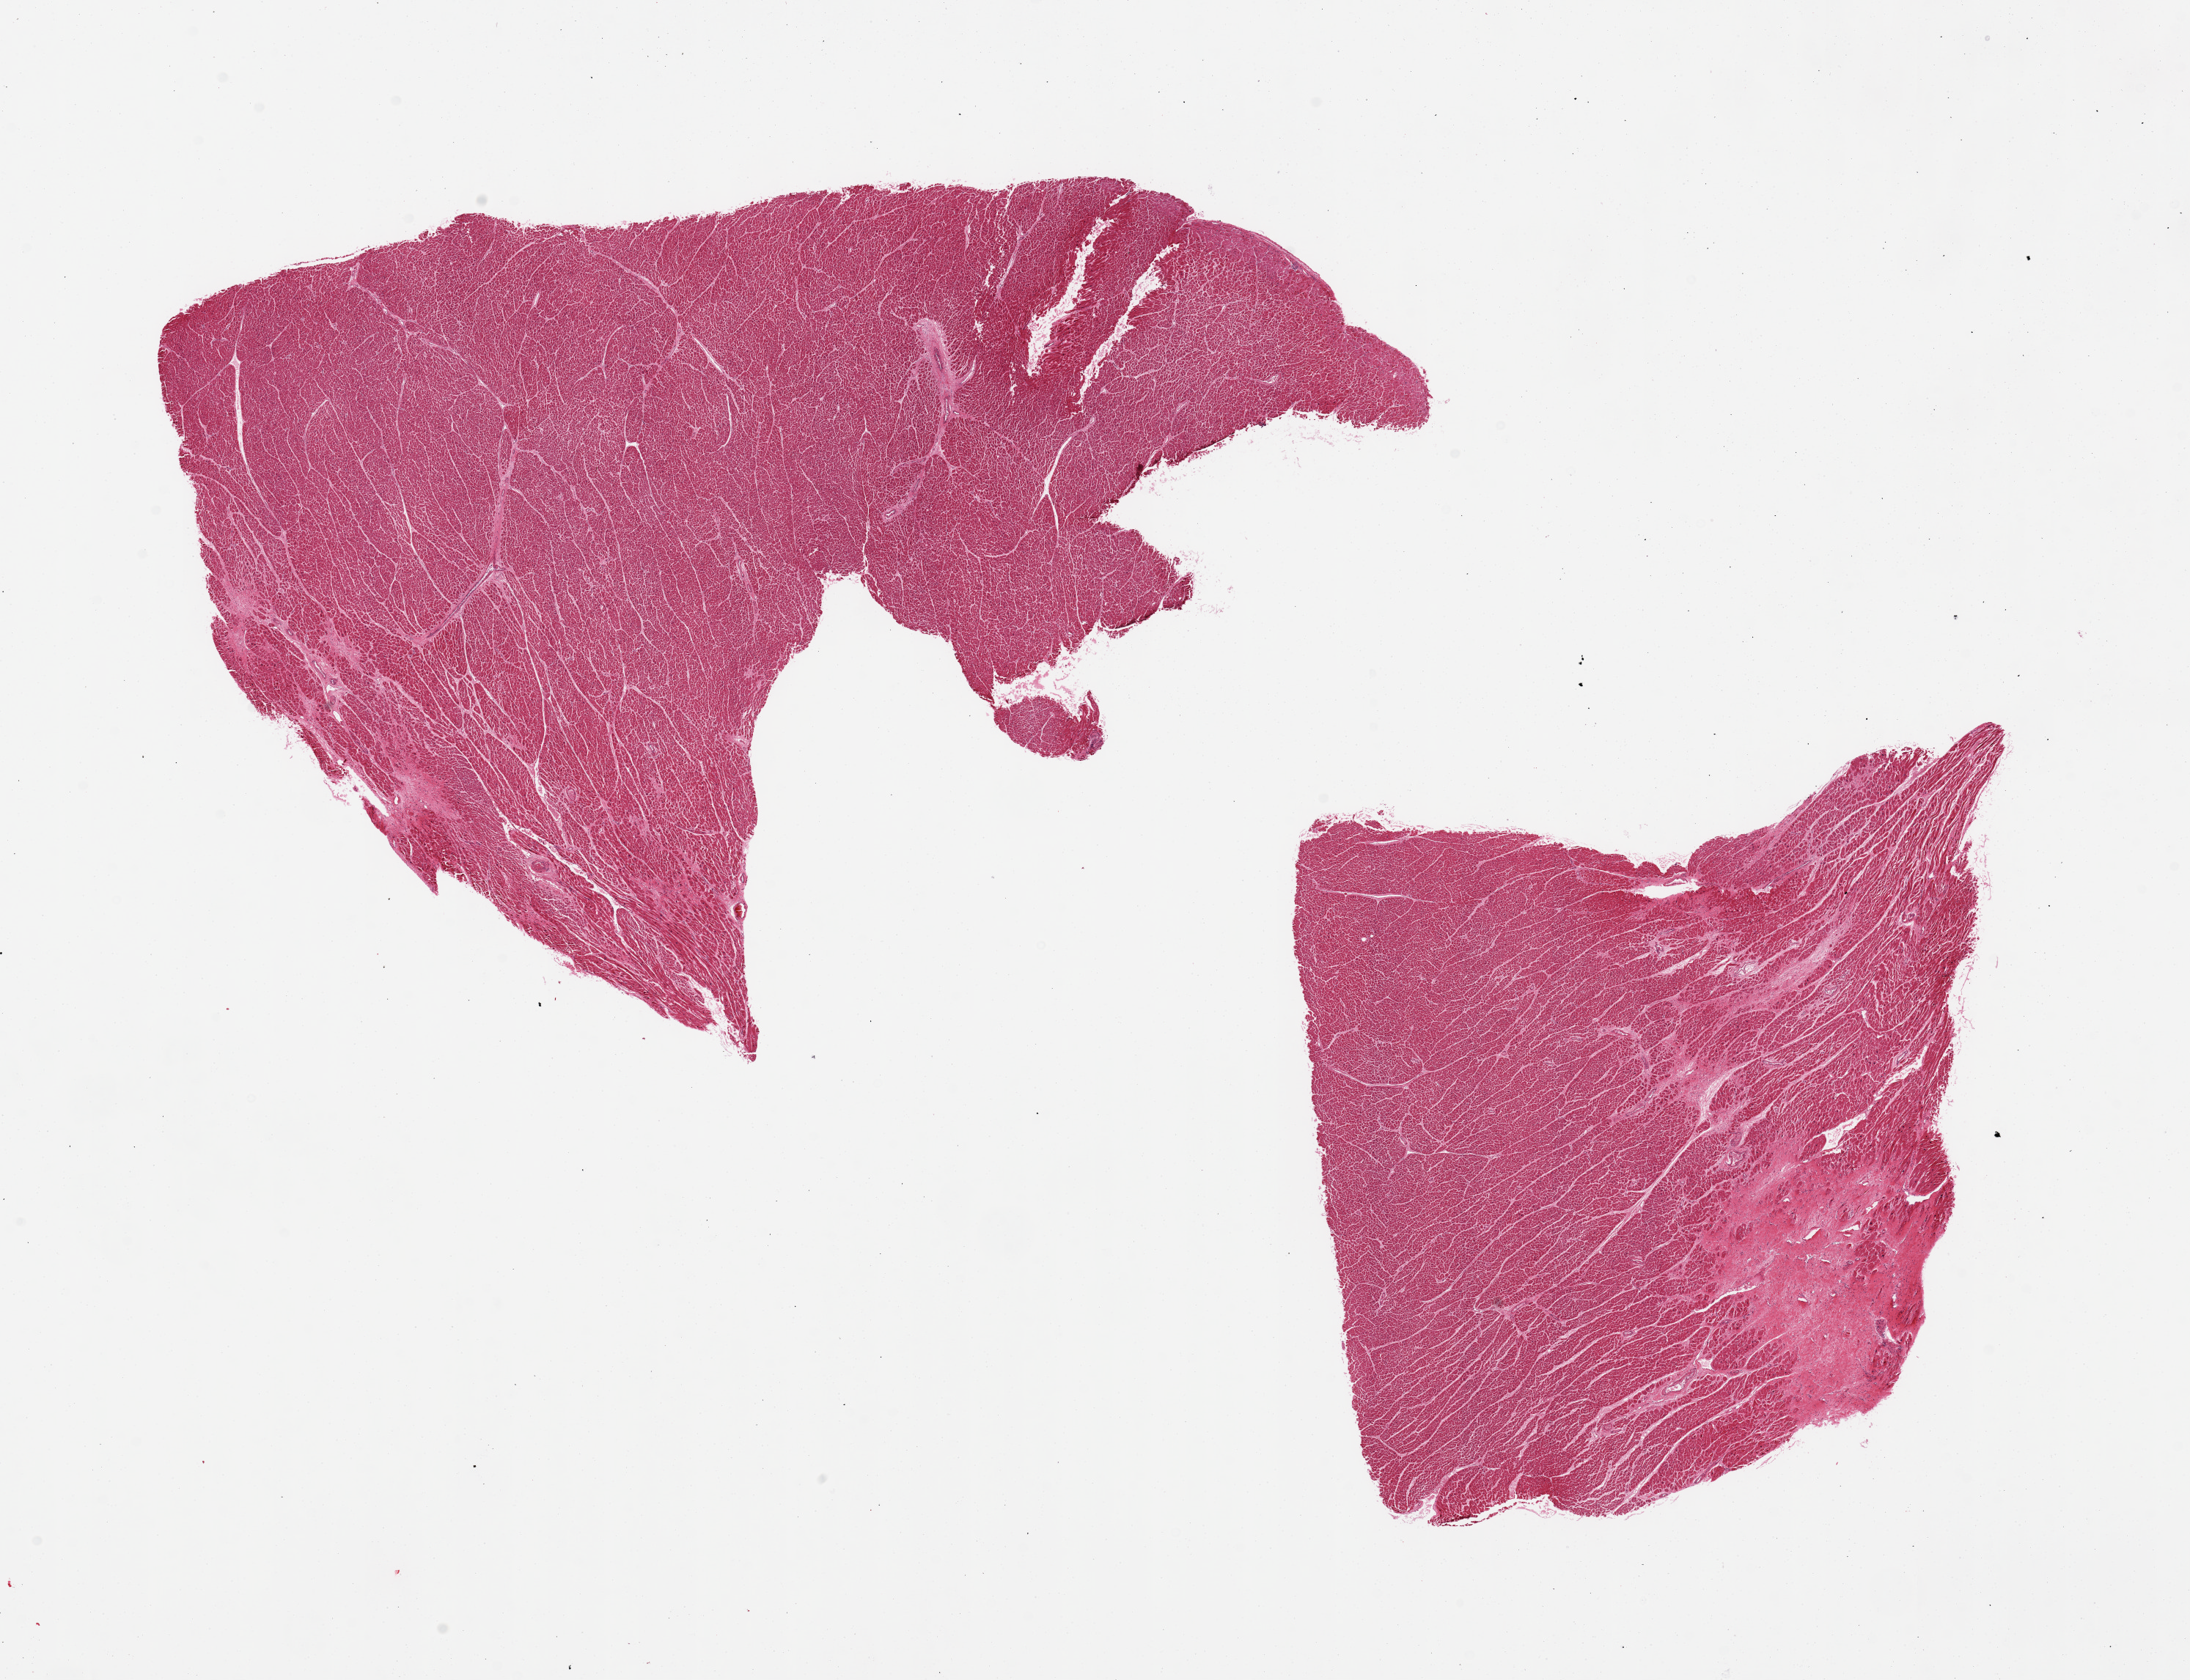
Digitized haematoxylin and eosin-stained section — shown as a low-resolution overview of the whole scanned area (about 23.6 x 18.1 mm). PAXgene-fixed, paraffin-embedded tissue. Sampled site (target tissue): heart. Tissue donor sample. Female donor.
* pathologist's review note for this sample: 2 pieces; 1 with patchy scars up to 2 sq mm; hypertrophied fibers